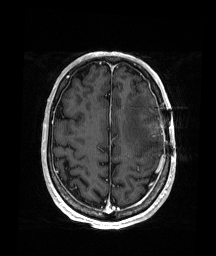
Brain MRI from a brain-tumour surgery series, one axial slice; slice 57 of 176 in the series (ordered by position); T1-weighted post-contrast; 1 mm slice thickness; 216 × 256 image matrix. From the clinical record (not read from this slice): histopathology: Glioblastoma; WHO grade: 4; IDH mutation: no.
Structures marked on this image (manually delineated by an expert):
- tumour: bounding box <145,123,160,135> (left, top, right, bottom; pixels)